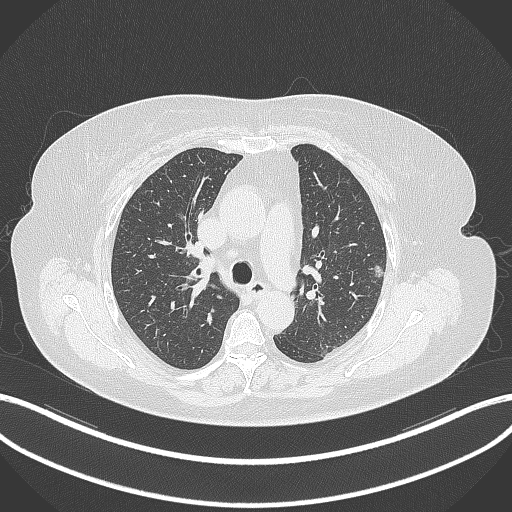
Chest CT, one axial slice; position 214 of 309 along the scan axis; lung window (W 1500 / L -600 HU); 1 mm slice thickness; 512 × 512 image matrix, field of view 400 × 400 mm. Patient: female, 70 years. Case-level facts recorded for this patient, not image findings: clinical TNM (as recorded): T1c N0 M0.
Annotated regions visible in this slice (rectangle marked by the reading radiologist):
- lung tumour (recorded histology: adenocarcinoma): bounding box [x1, y1, x2, y2] px = [365, 263, 387, 281]